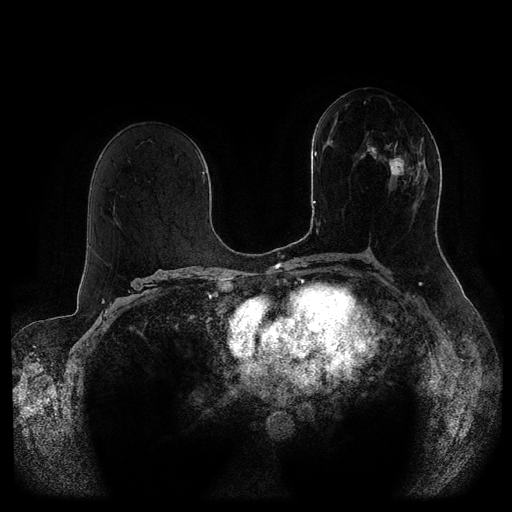
Breast MRI (dynamic contrast-enhanced, multi-phase), one axial slice; slice 52 of 116 in the series (ordered by position); dynamic contrast-enhanced series, time point 2 of 5 at this slice position (early post-contrast); 1.5 T; TE 2.6 ms, TR 5.3 ms; 2 mm slice thickness; 512 × 512 image matrix, field of view 370 × 370 mm. Female patient, age 51 years.
Outlined on this slice (semi-automatic segmentation, software-assisted and operator-edited):
- breast lesion (labelled 'tumour' in the annotation; benign lesions carry a separate 'benign' label): bounding box <360,137,427,184> (left, top, right, bottom; pixels)